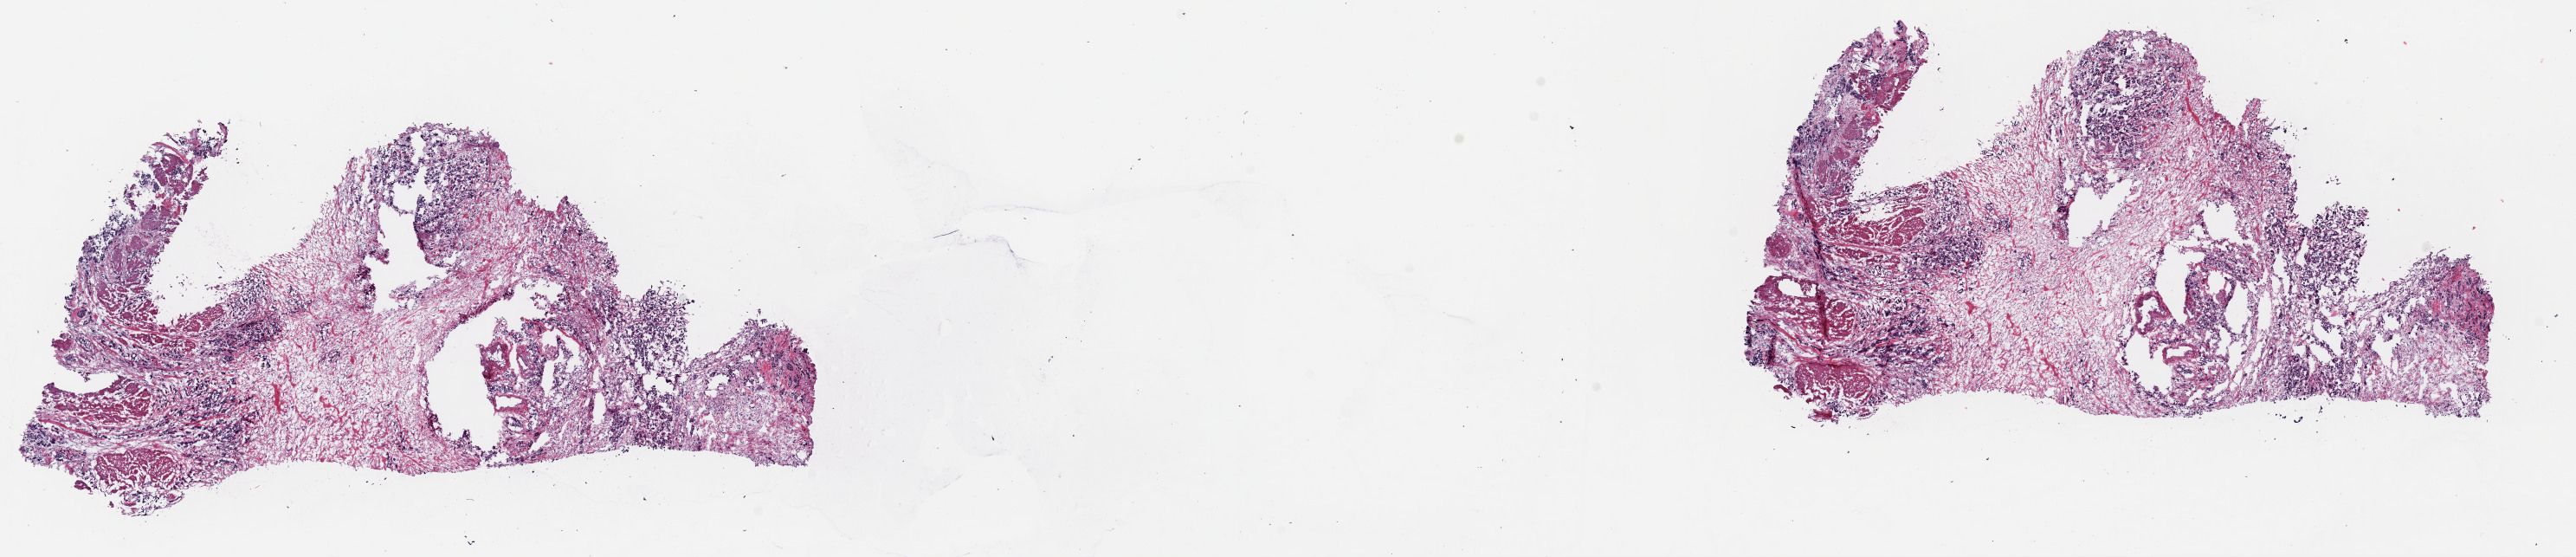
H&E-stained whole-slide image, shown as a low-resolution overview of the whole scanned area (about 23.5 x 5.1 mm, slide scanned at 40x). Frozen section from the top of the tissue portion. Primary tumour sample from the bladder. Female, age 79 years at initial diagnosis. Histologic grade: high grade. Composition of this section per pathologist review: tumour cells 85%, tumour nuclei 65%, normal cells 5%, stromal cells 10%, necrosis 0%. Inflammatory infiltration, as recorded: lymphocyte infiltration 0%, monocyte infiltration 0%, neutrophil infiltration 0%.
* pathologic diagnosis: Transitional cell carcinoma (trigone of bladder)
* AJCC pathologic stage: IV (6th edition)